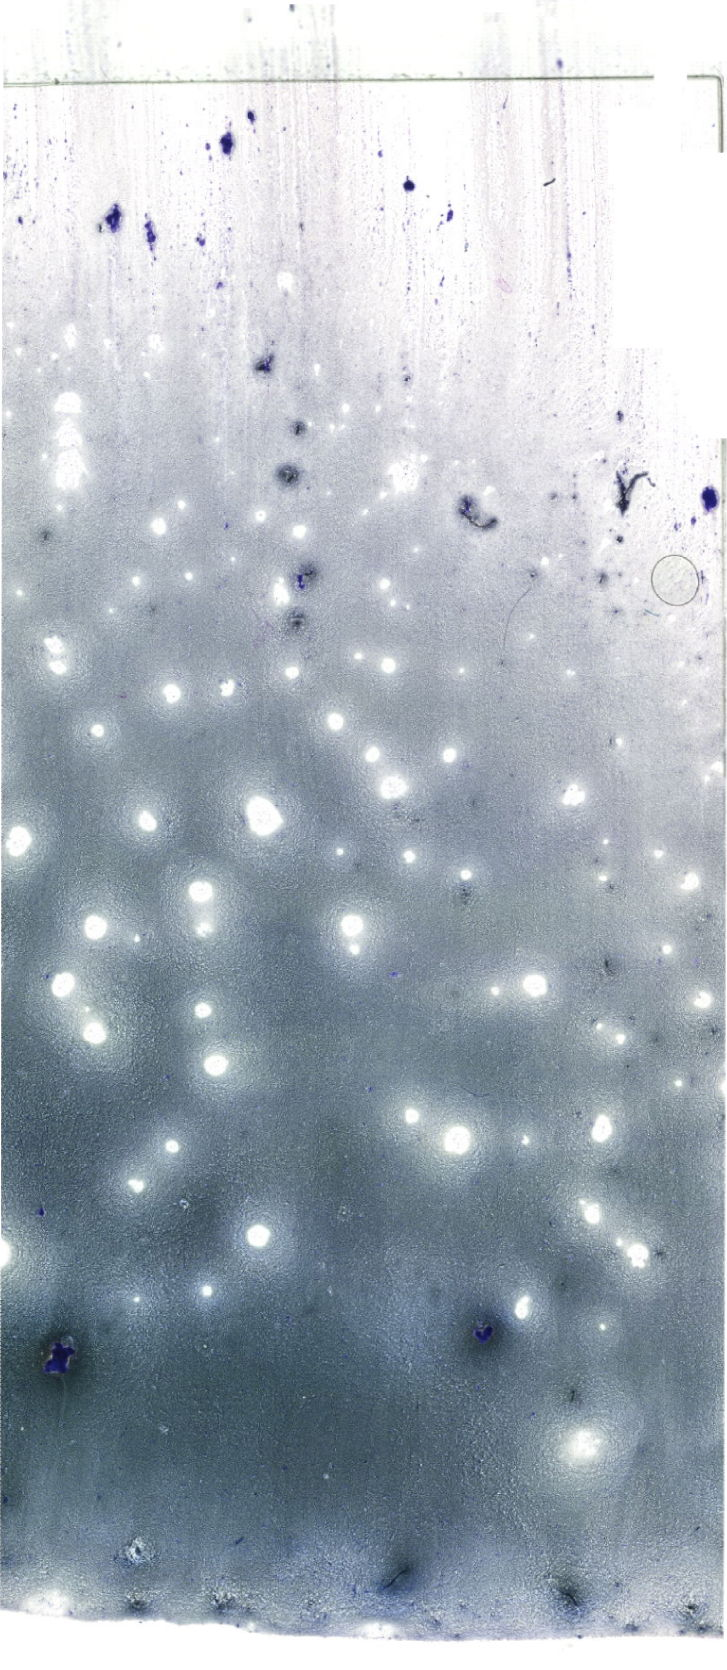
May-Grünwald–Giemsa-stained marrow aspirate smear (whole slide) — low-resolution overview of the scanned area, about 20.6 x 47.3 mm. Patient sex: female.
Diagnosis: Acute Promyelocytic Leukemia with t(15;17)(q24.1;q21.2);PML-RARA.